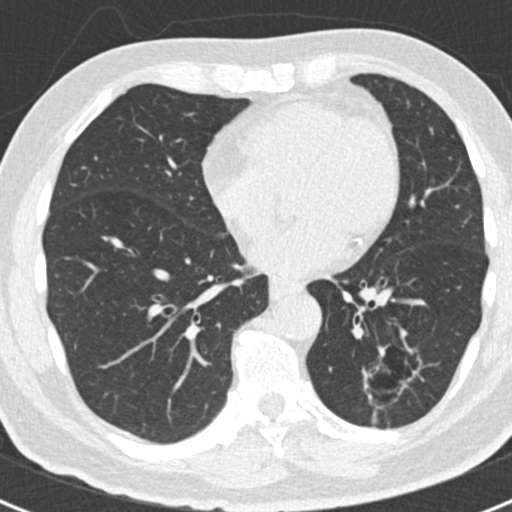
Low-dose screening chest CT, axial slice; baseline screening round; lung window (W 1500 / L -600 HU); standard (soft-tissue) reconstruction kernel (B30f); 120 kVp; slice 102 of 188 in the series; 512 × 512 image matrix. Male, age 66 years at enrolment.
Lesion marked by an expert reader, box from (x=342, y=338) to (x=419, y=416) px. The exam's reader record, not a measurement of the box and not confirmed to be the same lesion: non-calcified nodule or mass ≥4 mm, left lower lobe, 43 × 27 mm, smooth margins. Official screen result: positive, change unspecified: nodule(s) >= 4 mm or enlarging nodule(s), mass(es), or other non-specific abnormalities suspicious for lung cancer. Later outcome: lung cancer diagnosed 801 days after this screen — adenocarcinoma, NOS, left lower lobe, poorly differentiated (G3), stage IB (AJCC 6th edition), 38 mm at pathology.